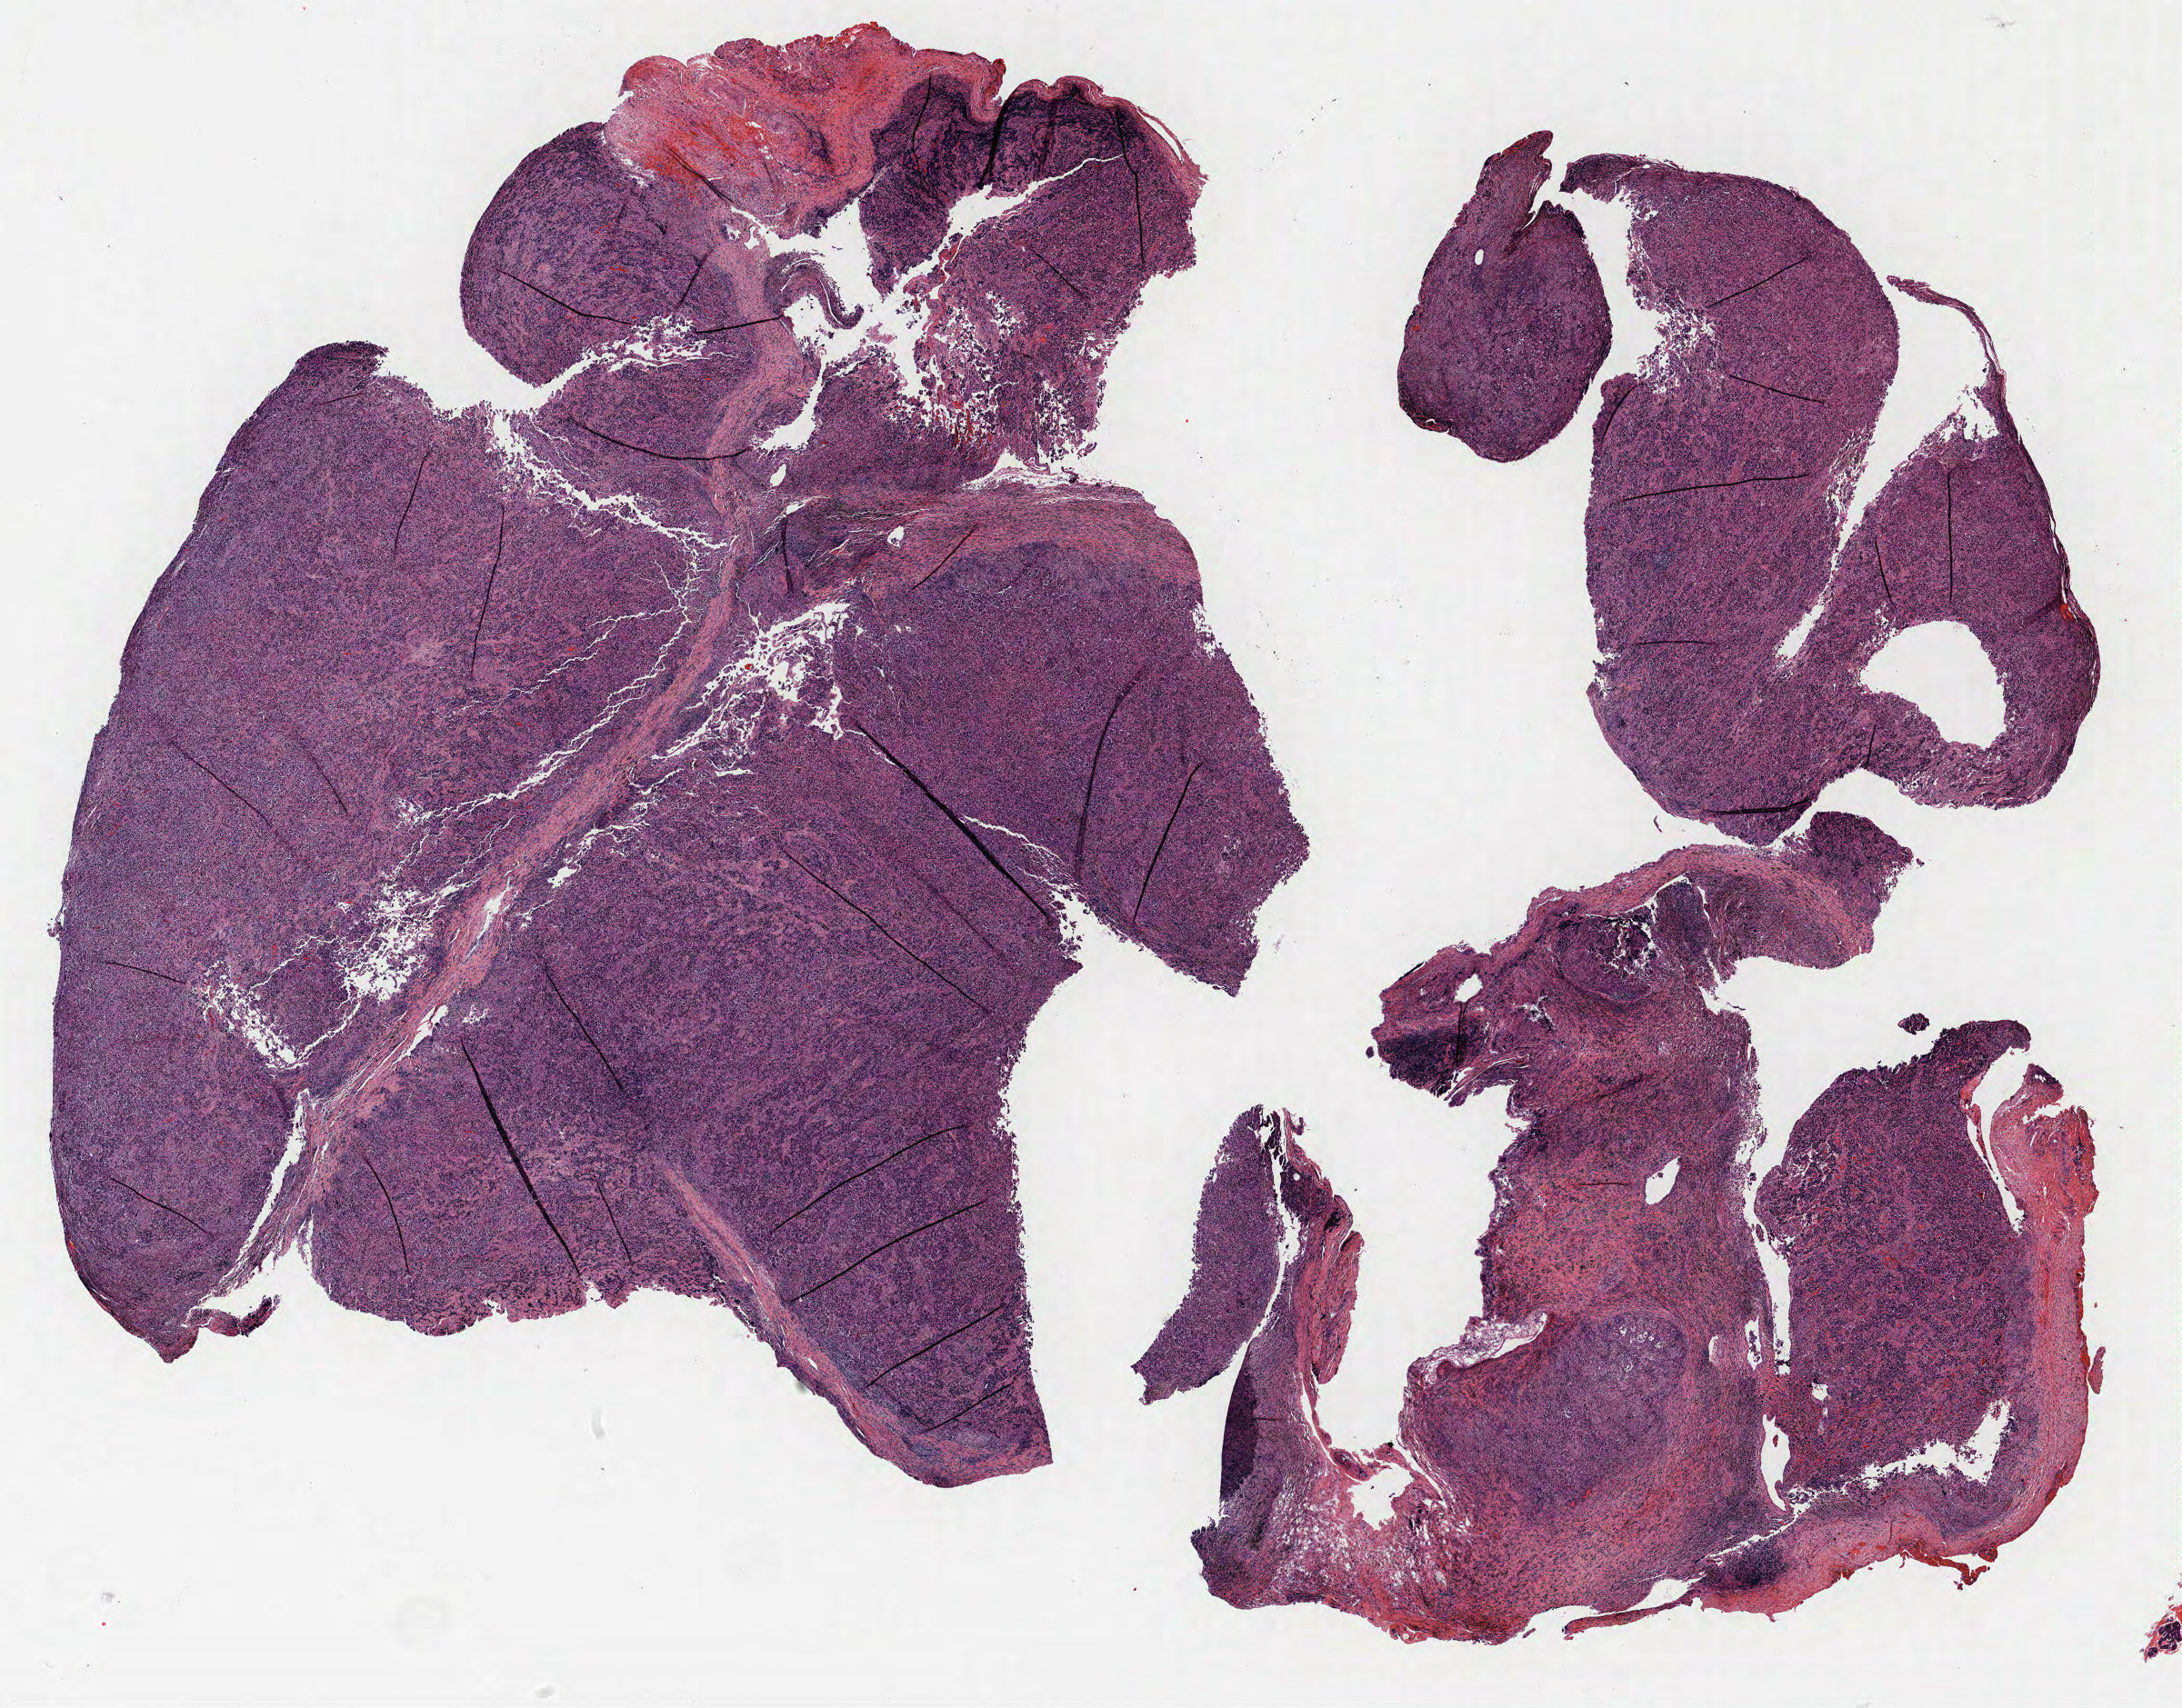
Whole-slide histology image, H&E-stained — shown as a low-resolution overview of the whole scanned area (about 19.2 x 15.0 mm), FFPE section, lung tissue. Male, age 67 at enrolment. Current smoker at enrolment. Grade: poorly differentiated (G3).
Participant's lung-cancer diagnosis: Adenocarcinoma, NOS. Tumour size (pathology): 18 mm. ICD-O-3 topography: upper lobe of lung (C34.1). Primary tumour location (clinical record): left upper lobe, left lower lobe. Stage (AJCC 6th edition): IIA.